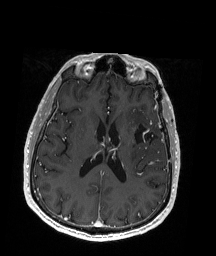
Brain MRI from a brain-tumour surgery series, one axial slice. Slice 84 of 192 in the series (ordered by position). T1-weighted post-contrast. 1 mm slice thickness. 216 × 256 image matrix, field of view 211 × 250 mm. Case-level facts recorded for this patient, not image findings: histopathology: Oligodendroglioma; WHO grade: 2; IDH mutation: yes; tumour location: Left Insular.
Annotated regions visible in this slice (outlined manually by an expert reader):
- previous resection cavity: bounding box (x1, y1, x2, y2) in pixels: (136, 121, 160, 148)